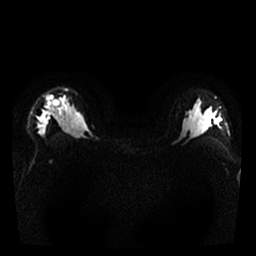
Breast MRI, one axial slice. Diffusion-weighted series; image 2 of 4 stored at this slice position (different b-values; order by instance number). 1.5 T. 4 mm slice thickness. 256 × 256 image matrix, field of view 320 × 320 mm. Female patient.
Structures marked on this image (outlined manually by an expert reader):
- tumour on diffusion-weighted imaging: bounding box <46,95,60,106> (left, top, right, bottom; pixels)